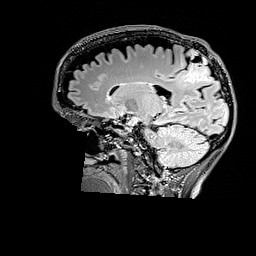
Brain MRI from a brain-tumour surgery series, one sagittal slice; position 105 of 176 along the scan axis; T2 FLAIR; 1 mm slice thickness; 256 × 256 image matrix, field of view 256 × 256 mm. From the clinical record (not read from this slice): histopathology: Astrocytoma; WHO grade: 3; IDH mutation: yes; tumour location: Right Parietal.
Annotated regions visible in this slice (manually delineated by an expert):
- tumour: bounding box <179,49,212,84> (left, top, right, bottom; pixels)
- tumour: <185,58,213,83>